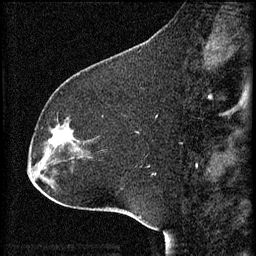
Breast MRI (dynamic contrast-enhanced), one sagittal slice. Position 21 of 60 along the scan axis. 3 images stored at this slice position (order not interpretable as contrast timing). 1.5 T. TE 4.2 ms, TR 8.2 ms. 2 mm slice thickness. 256 × 256 image matrix, field of view 180 × 180 mm. Female patient, age 32 years.
Annotated regions visible in this slice (semi-automatically segmented with operator editing):
- analysis volume of interest (the breast-tissue region the enhancement analysis was run in; not a lesion): bounding box <47,116,84,157> (left, top, right, bottom; pixels)
- tumour enhancement mask (voxels above the 70 % enhancement threshold inside the analysis volume of interest): <48,134,63,155>